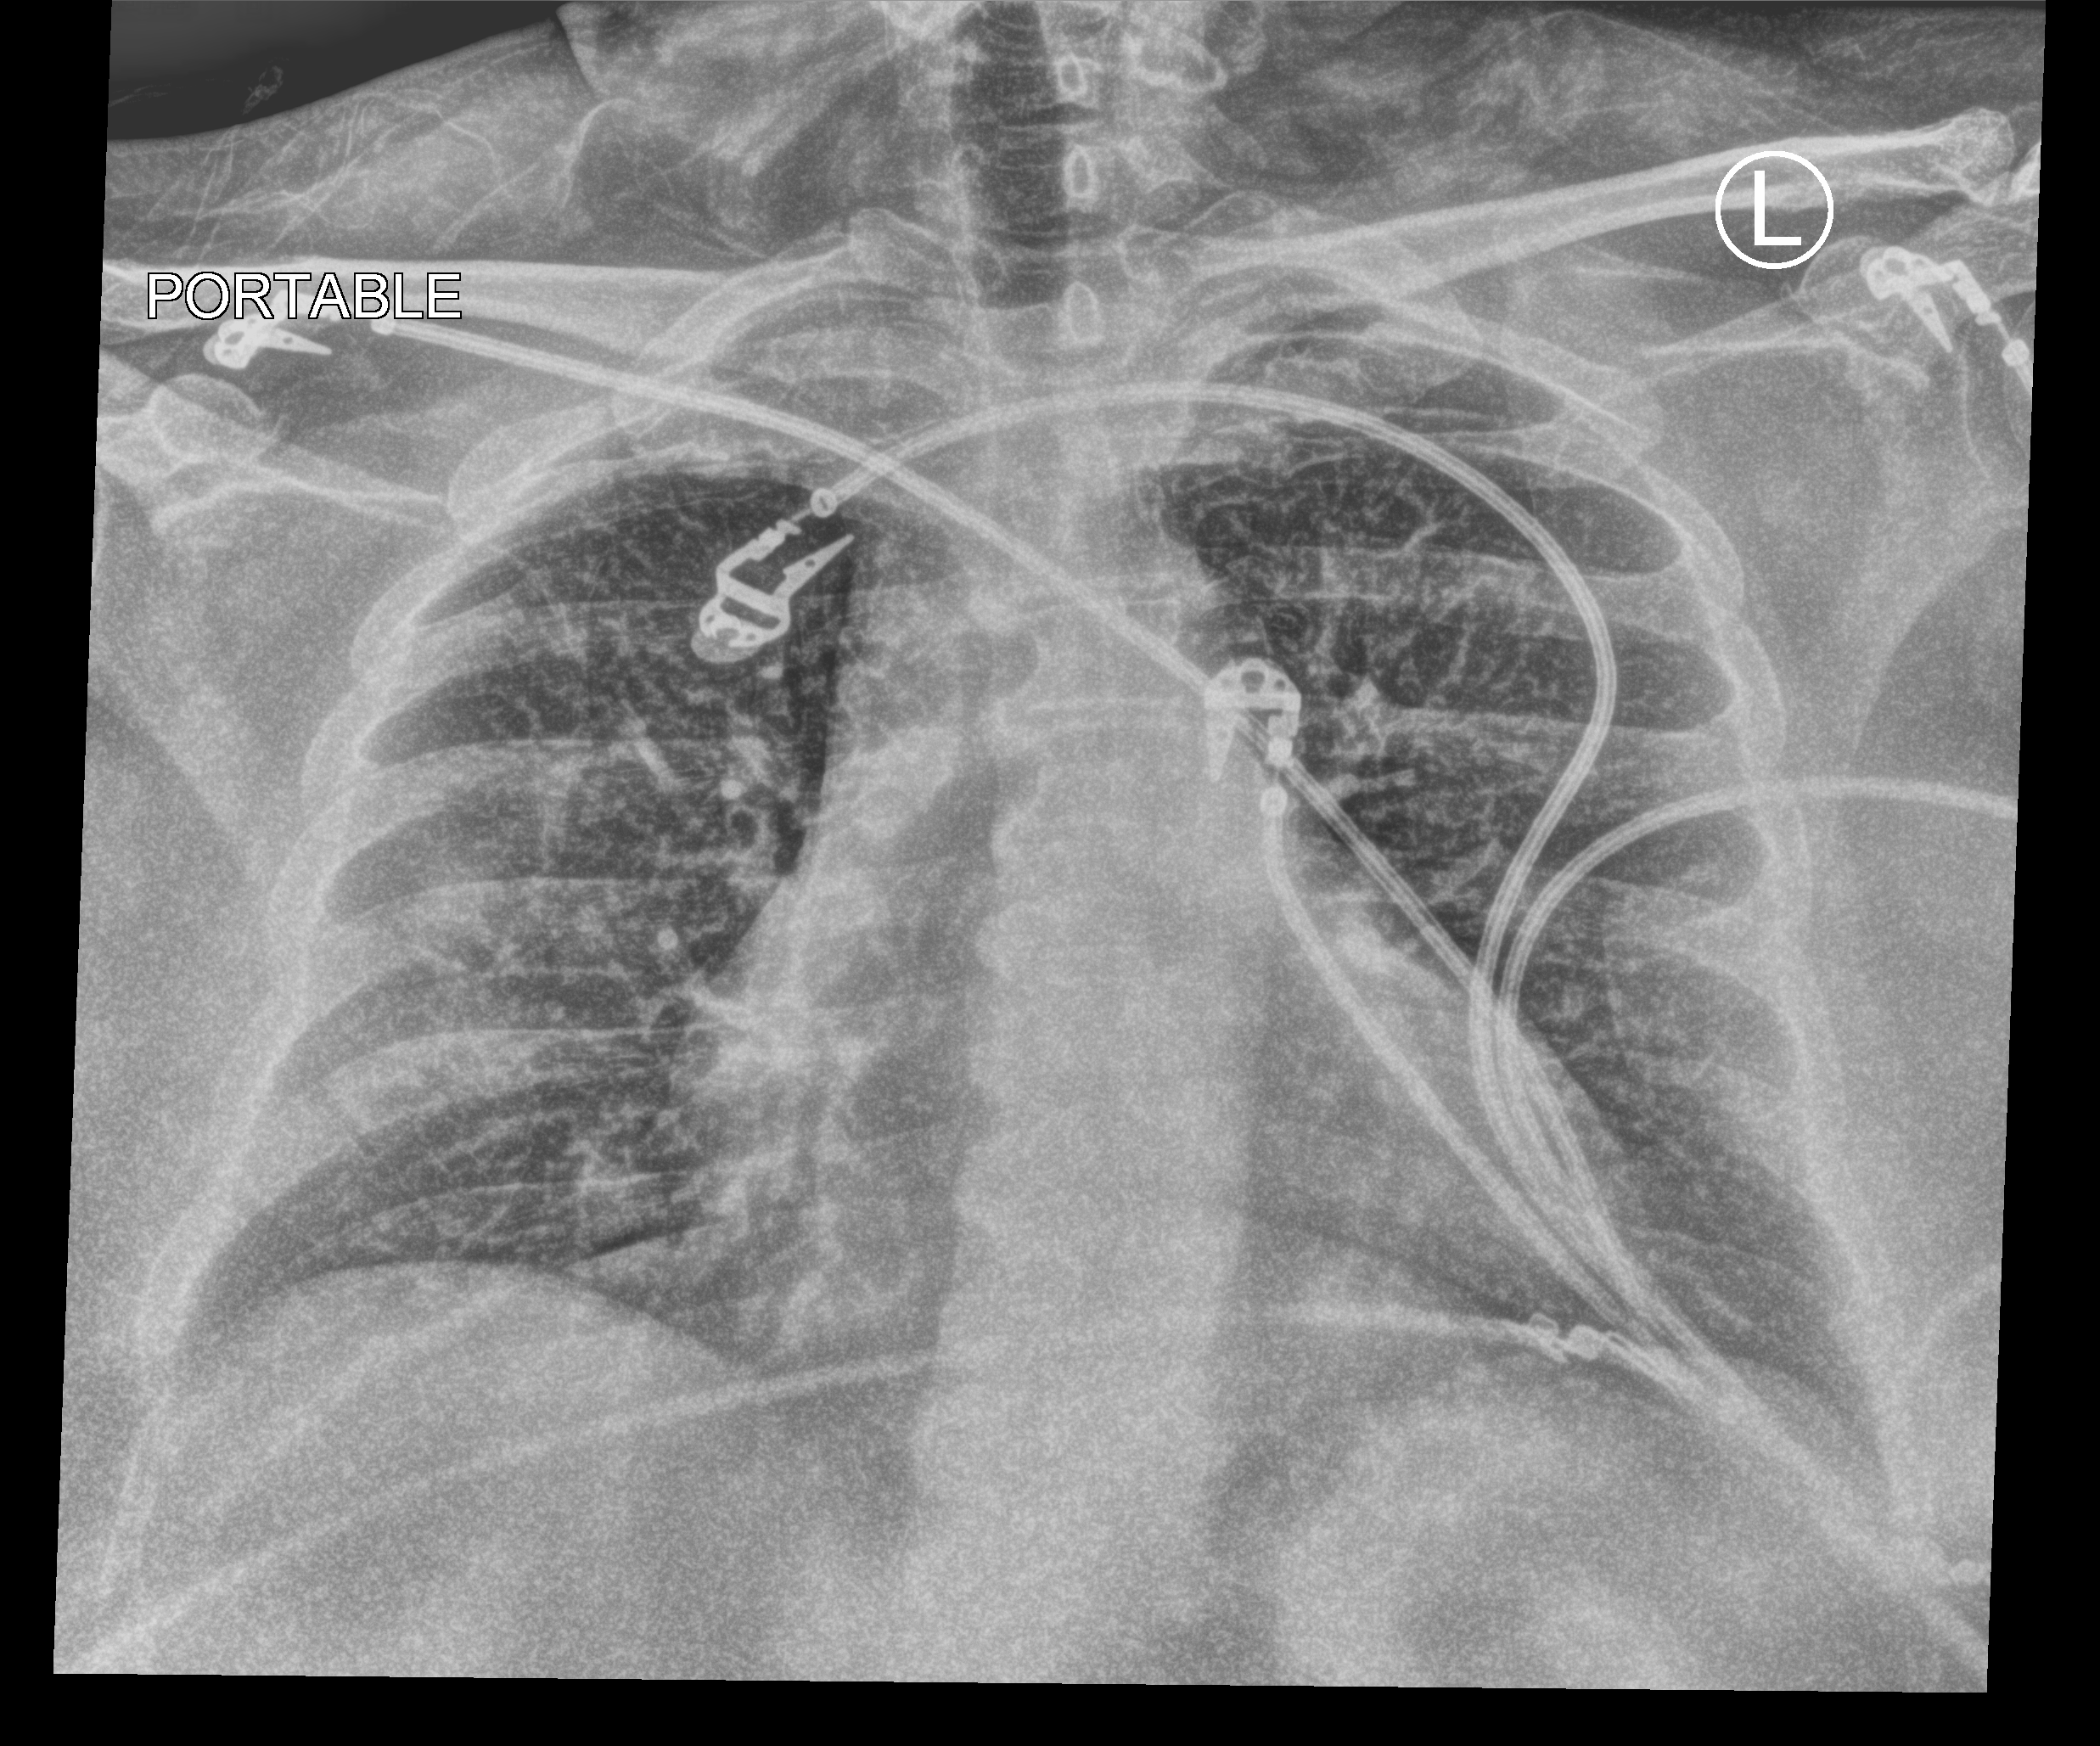
Chest X-ray (portable). Female patient hospitalised with COVID-19, age 18–59 years.
From the hospital-stay record, not from the radiograph (when in the stay this image was taken is not recorded):
- hypertension (admission record): yes